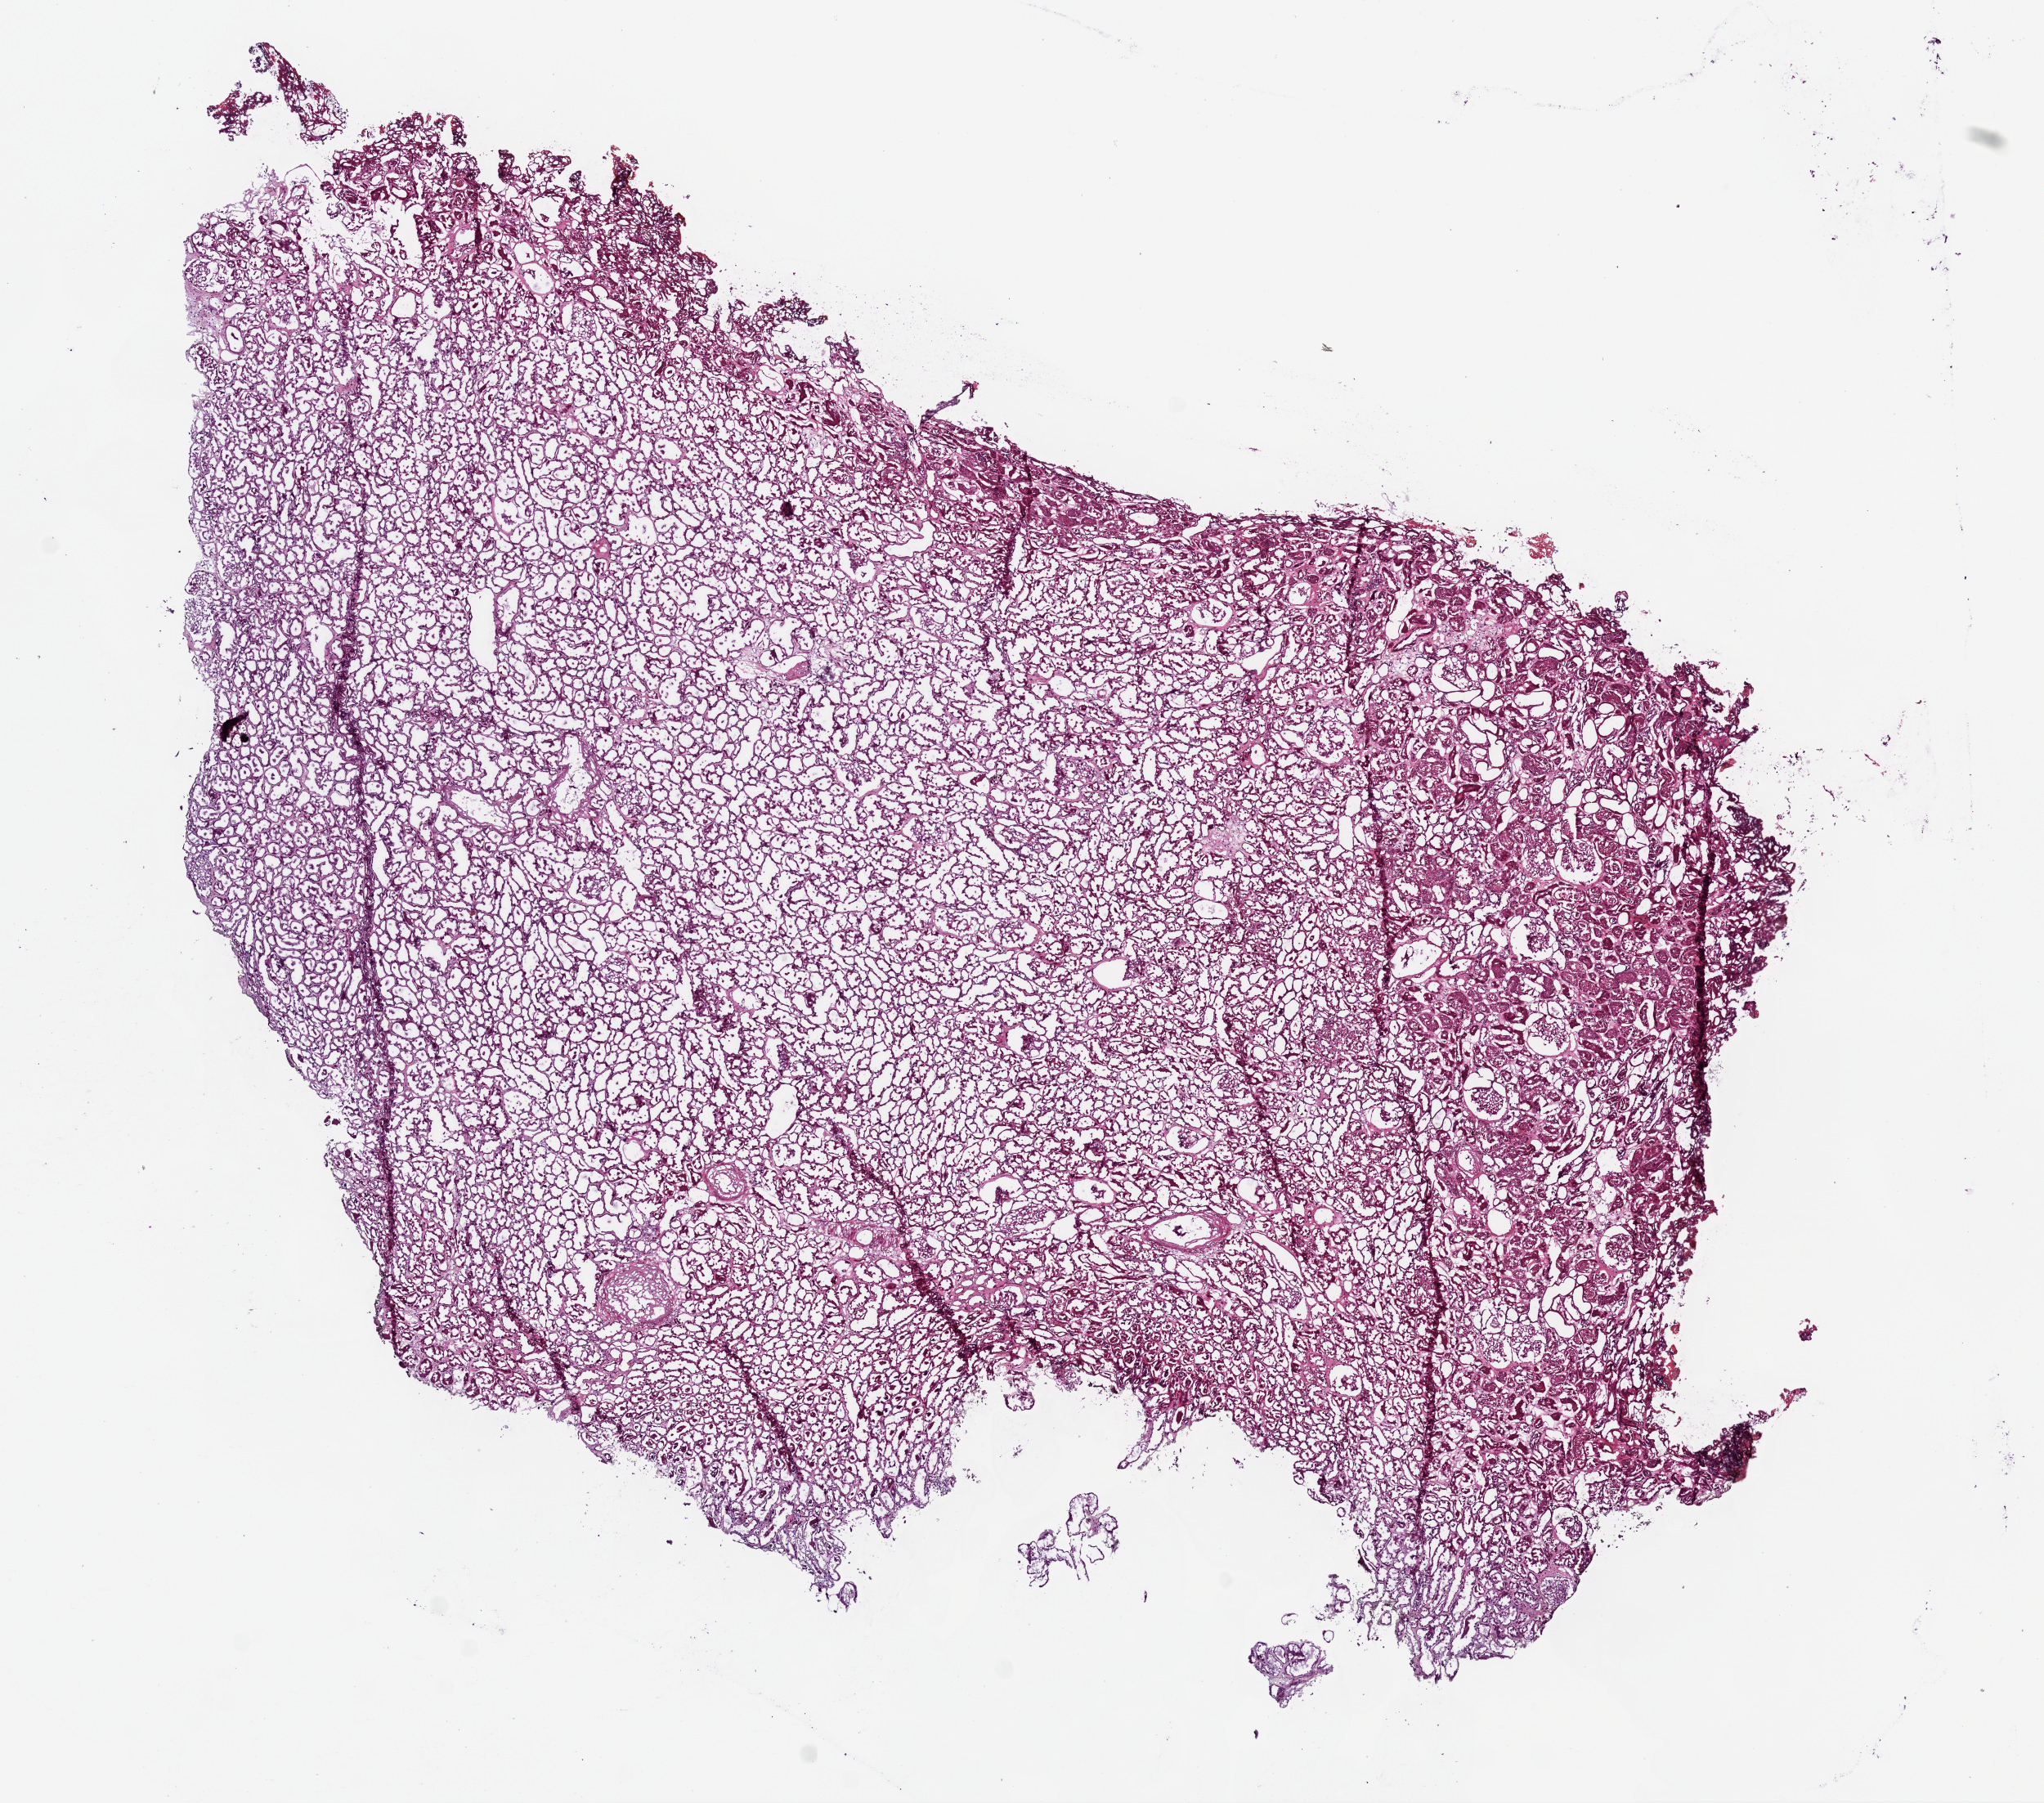
H&E whole-slide image — whole scanned area (about 10.0 x 8.8 mm, from a 20x scan) shown as a low-resolution overview; frozen section; sample: solid tissue normal (non-tumour tissue), kidney. Male, age 74 years at initial diagnosis.
This section: solid tissue normal sample (biorepository sample class). Patient diagnosis: Clear cell adenocarcinoma, NOS.